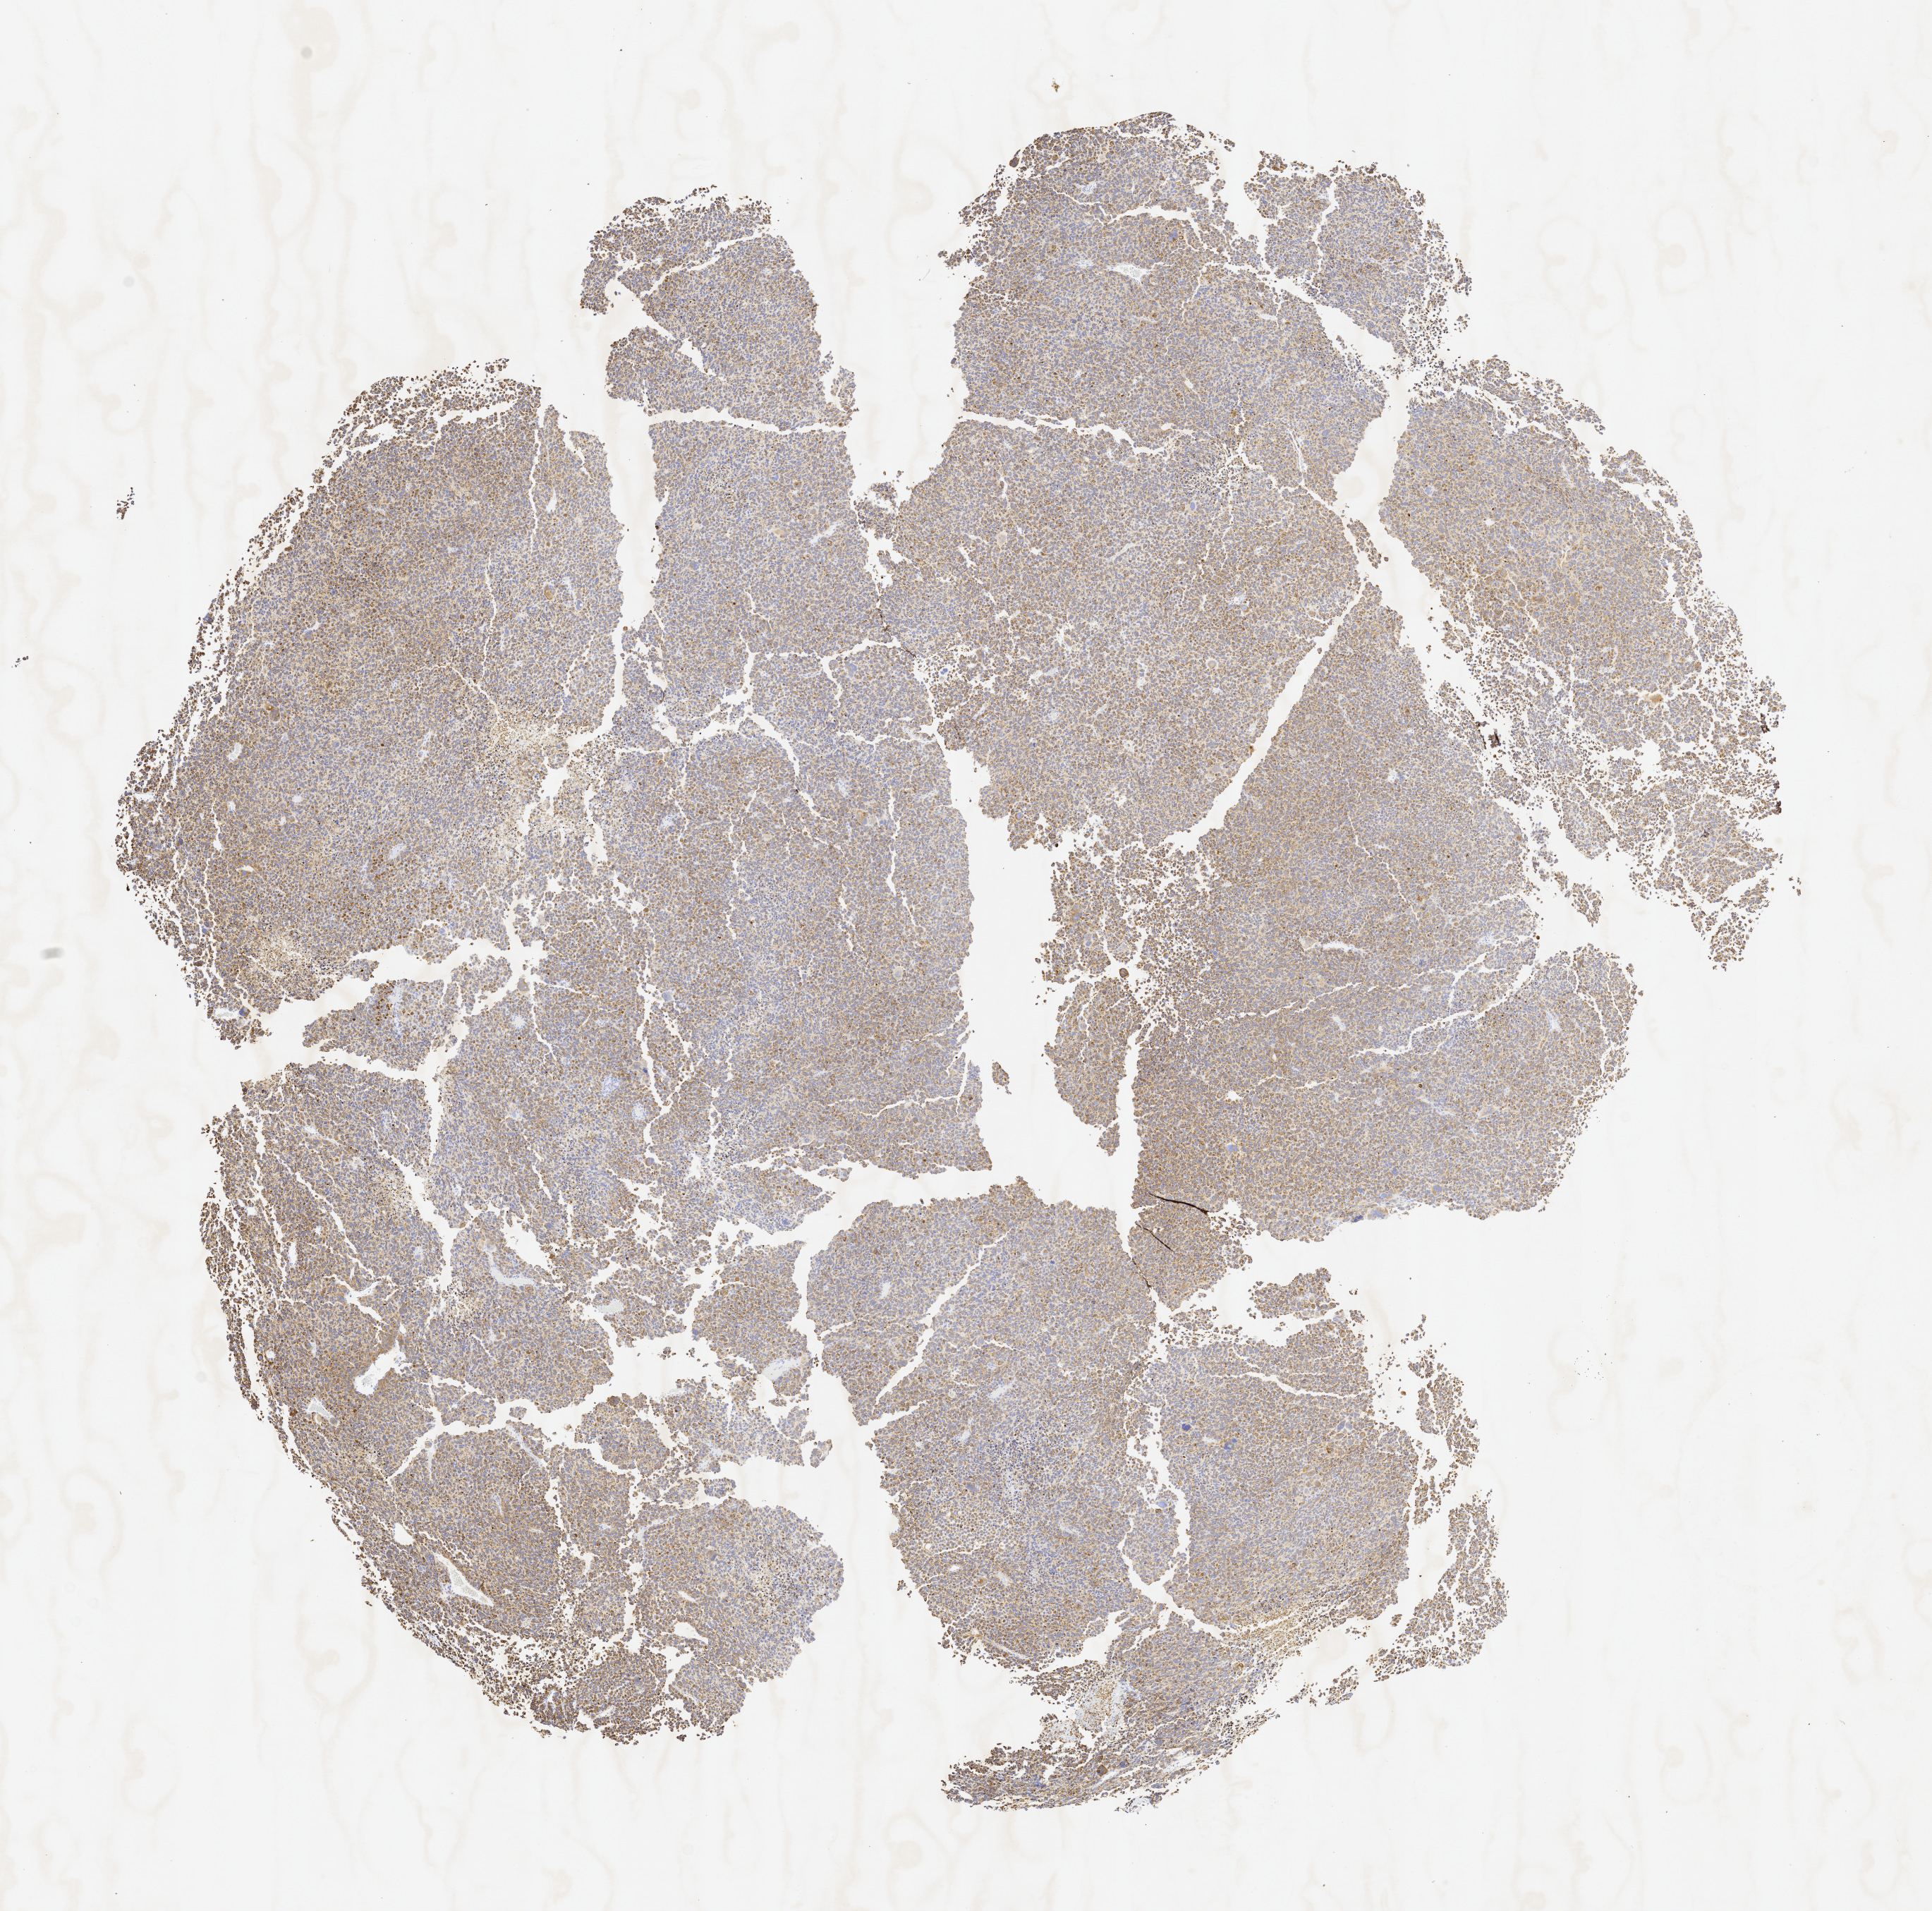
Whole-slide image, haematoxylin and eosin: patient-derived xenograft (human tumor grown in a mouse), passage 2 — low-resolution overview of the scanned area, about 11.0 x 10.9 mm; FFPE section; tumor site category: skin.
Originating patient diagnosis: Melanoma.